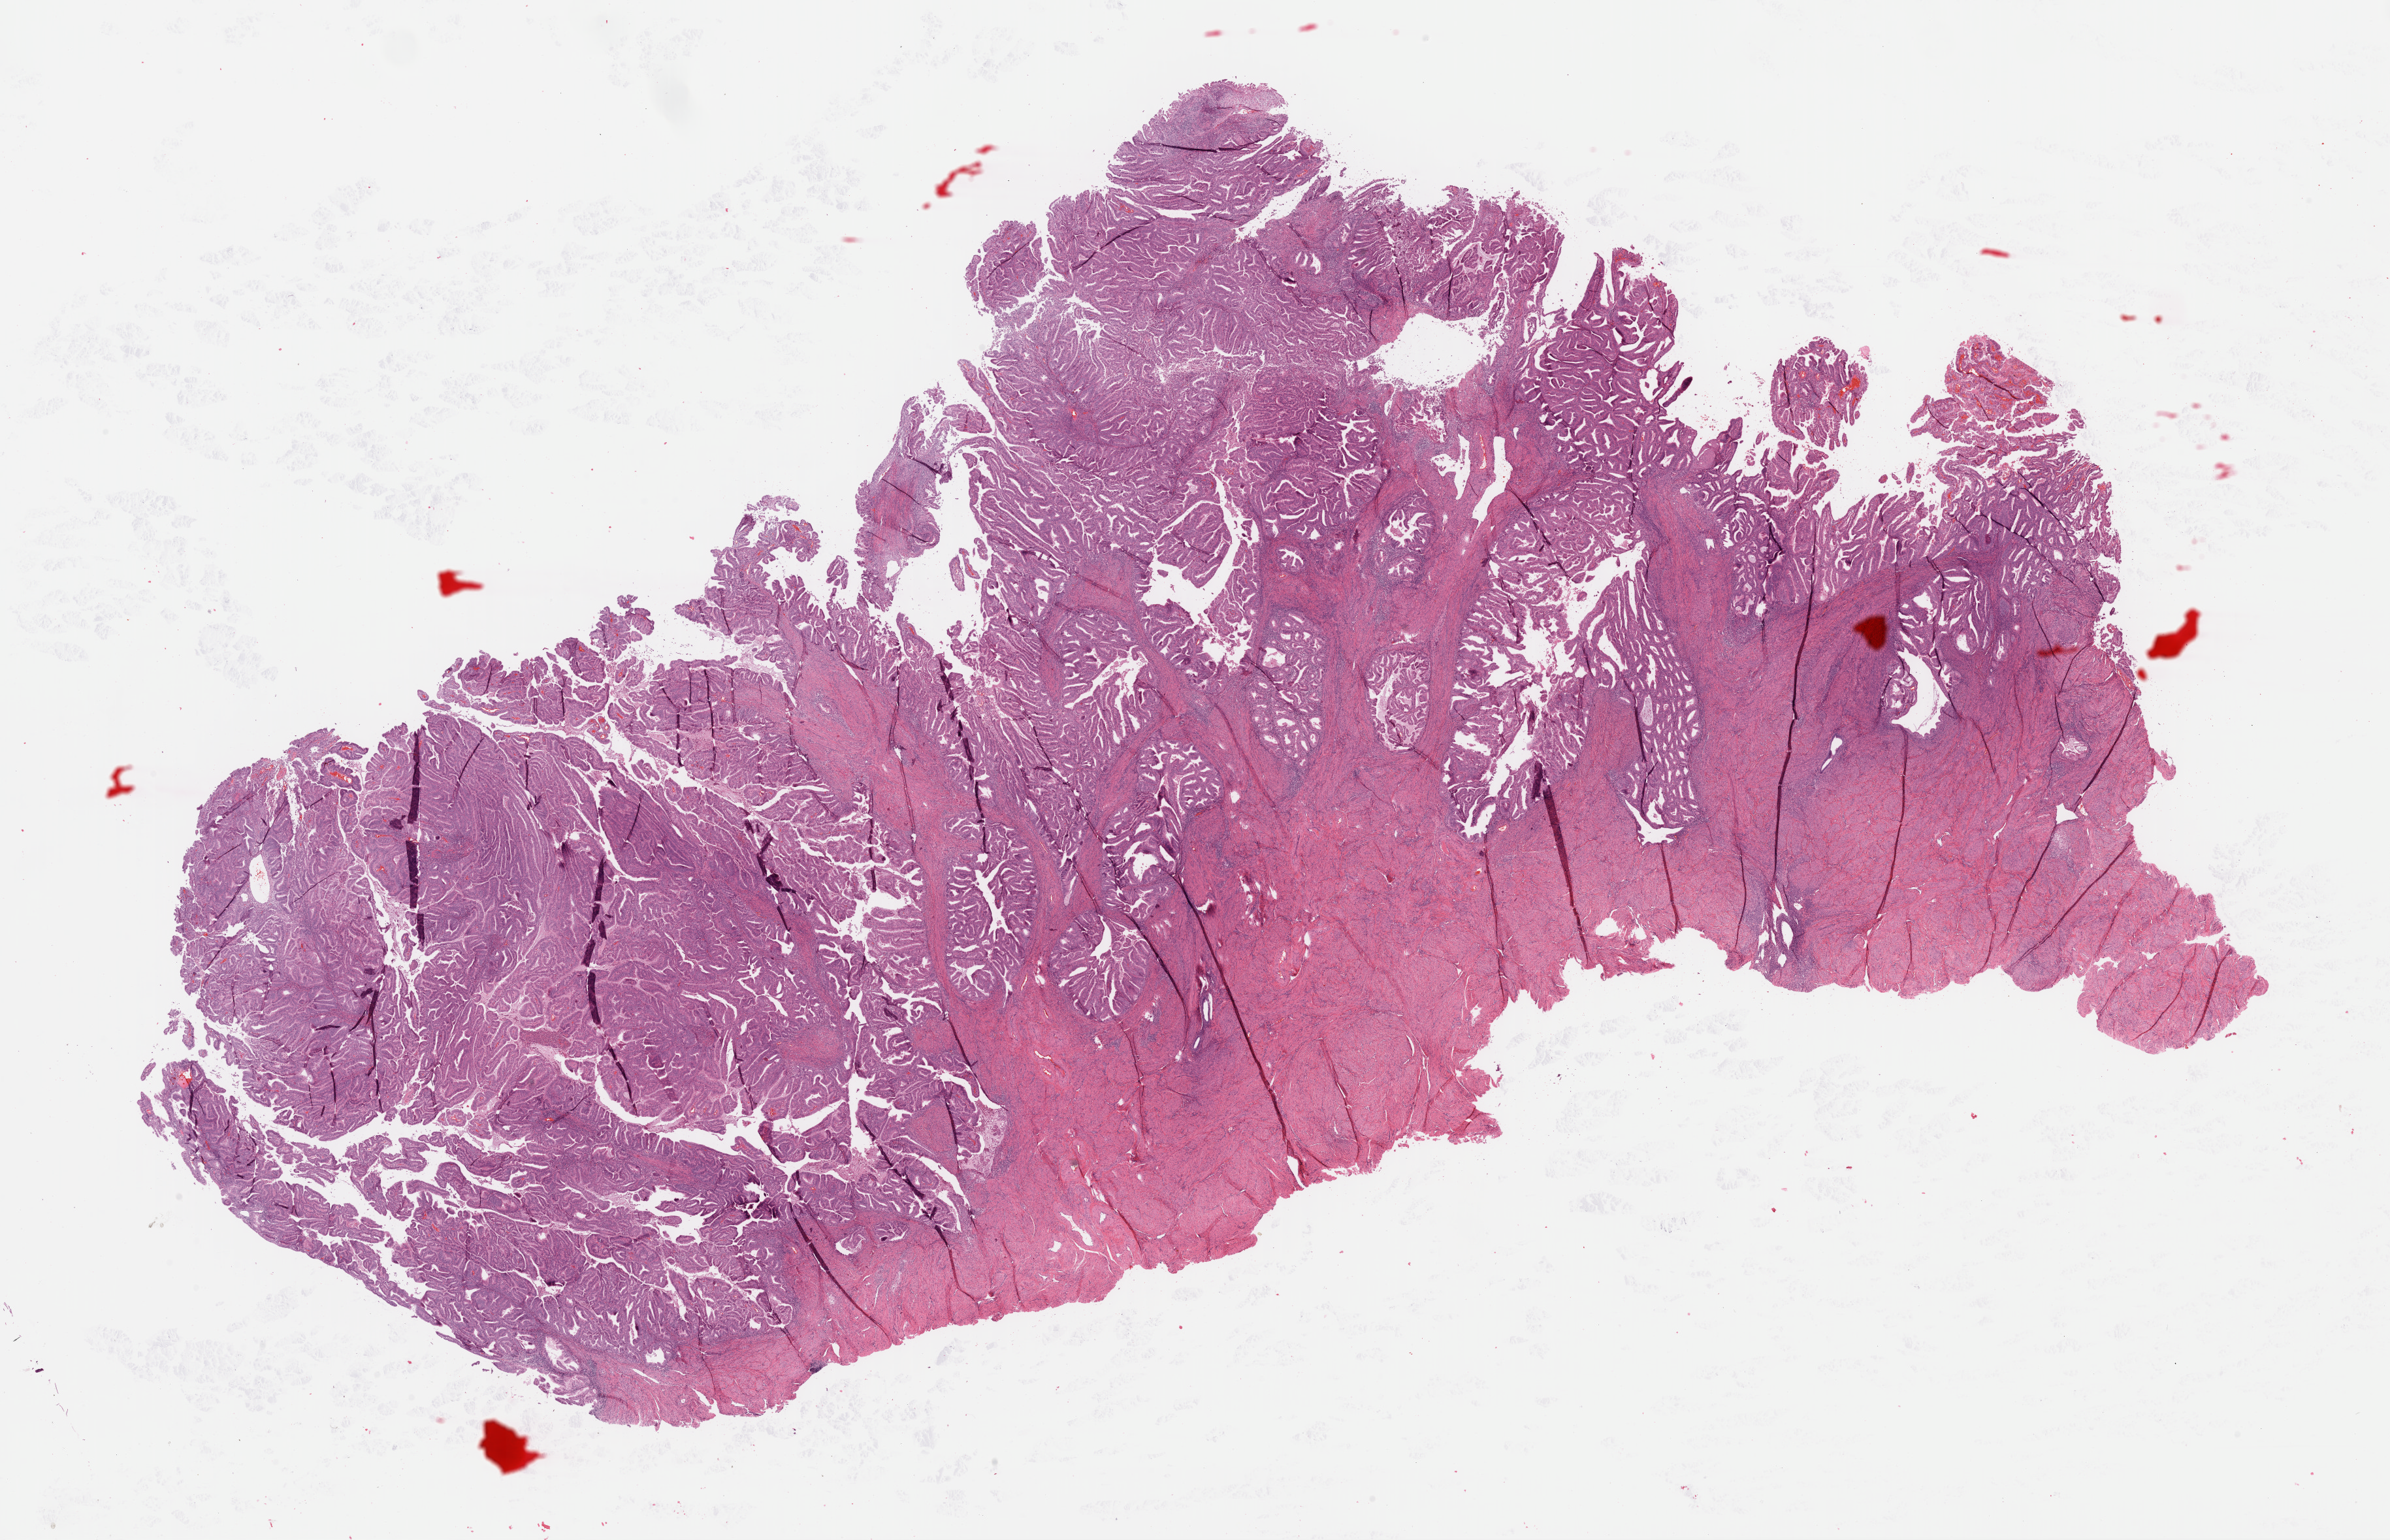
Digitized Hematoxylin and eosin (H&E) stained tissue section (whole slide), a low-resolution overview of the entire scanned area, about 28.9 x 18.6 mm (slide scanned at 40x). Formalin-fixed paraffin-embedded (FFPE) diagnostic section. Sample: primary tumour, uterus. Female, age 57 years at initial diagnosis.
Histologic diagnosis: Endometrioid adenocarcinoma, NOS (endometrium).